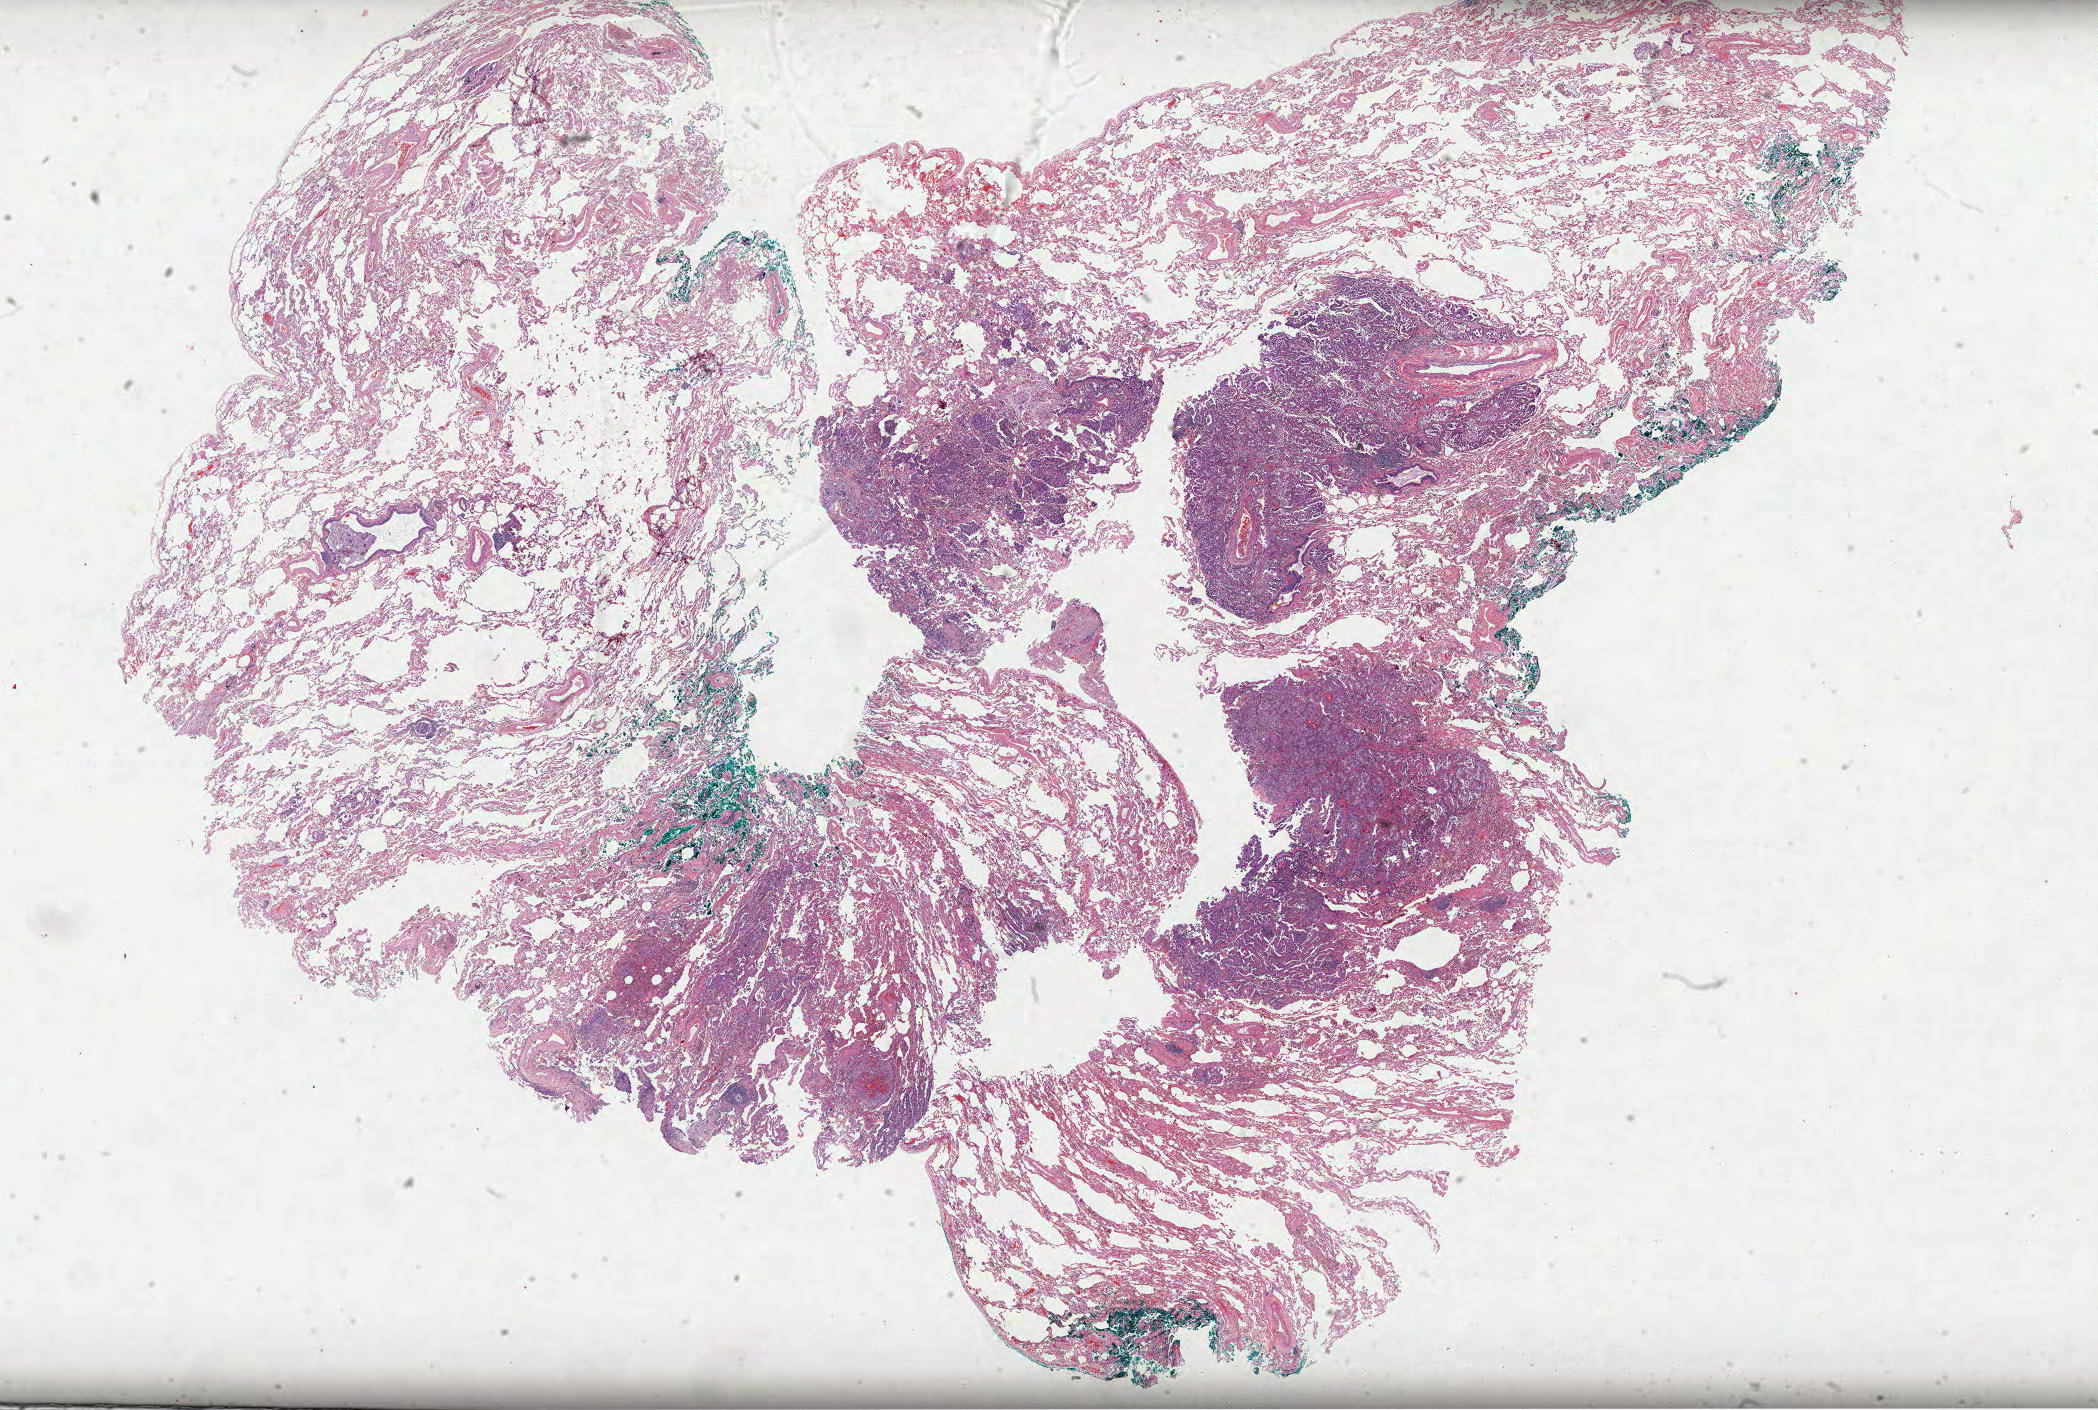
Hematoxylin and eosin (H&E) stained whole-slide image, whole scanned area (about 33.8 x 22.7 mm) shown as a low-resolution overview, formalin-fixed paraffin-embedded (FFPE) diagnostic section, lung, primary tumour sample. Patient: male, age at initial diagnosis 70 years.
Histologic diagnosis: Adenocarcinoma, NOS (upper lobe, lung).